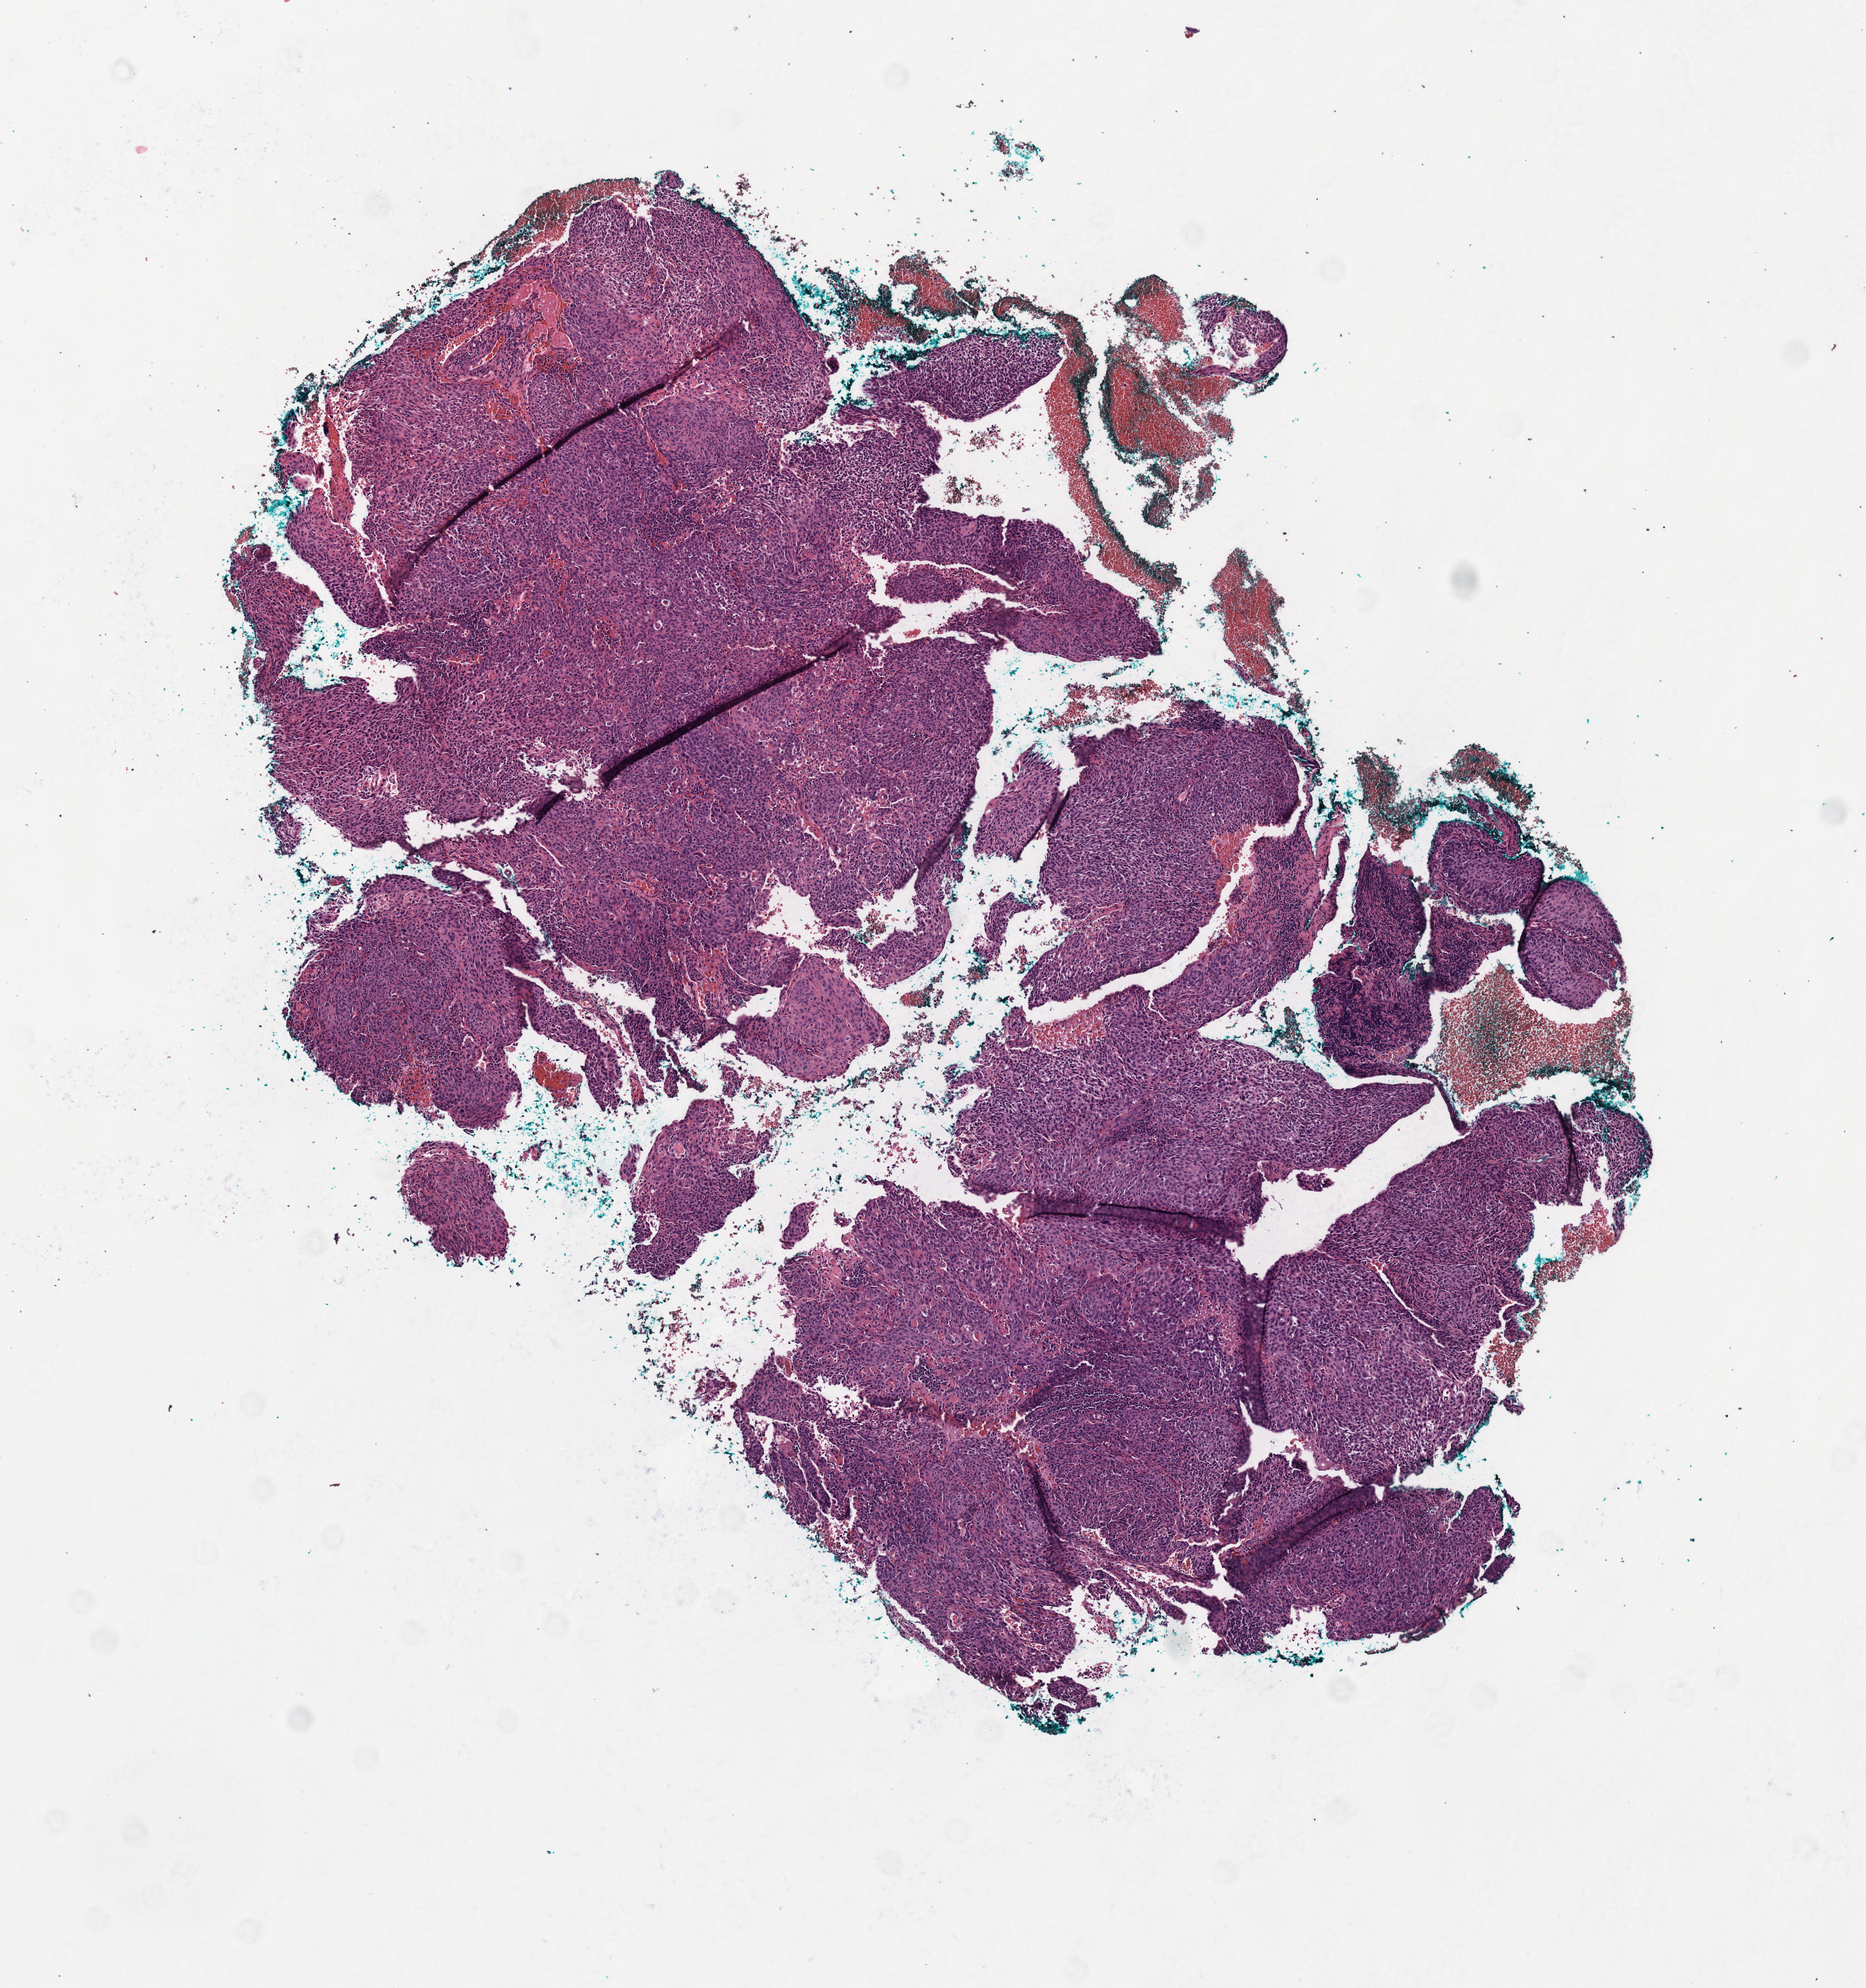
Digitized H&E-stained tissue section (whole slide) — a low-resolution overview of the entire scanned area, about 5.5 x 5.9 mm; formalin-fixed paraffin-embedded (FFPE) diagnostic section; cervix, primary tumour sample. Female, age 29 years at initial diagnosis.
Histologic diagnosis: Squamous cell carcinoma, NOS (cervix uteri).